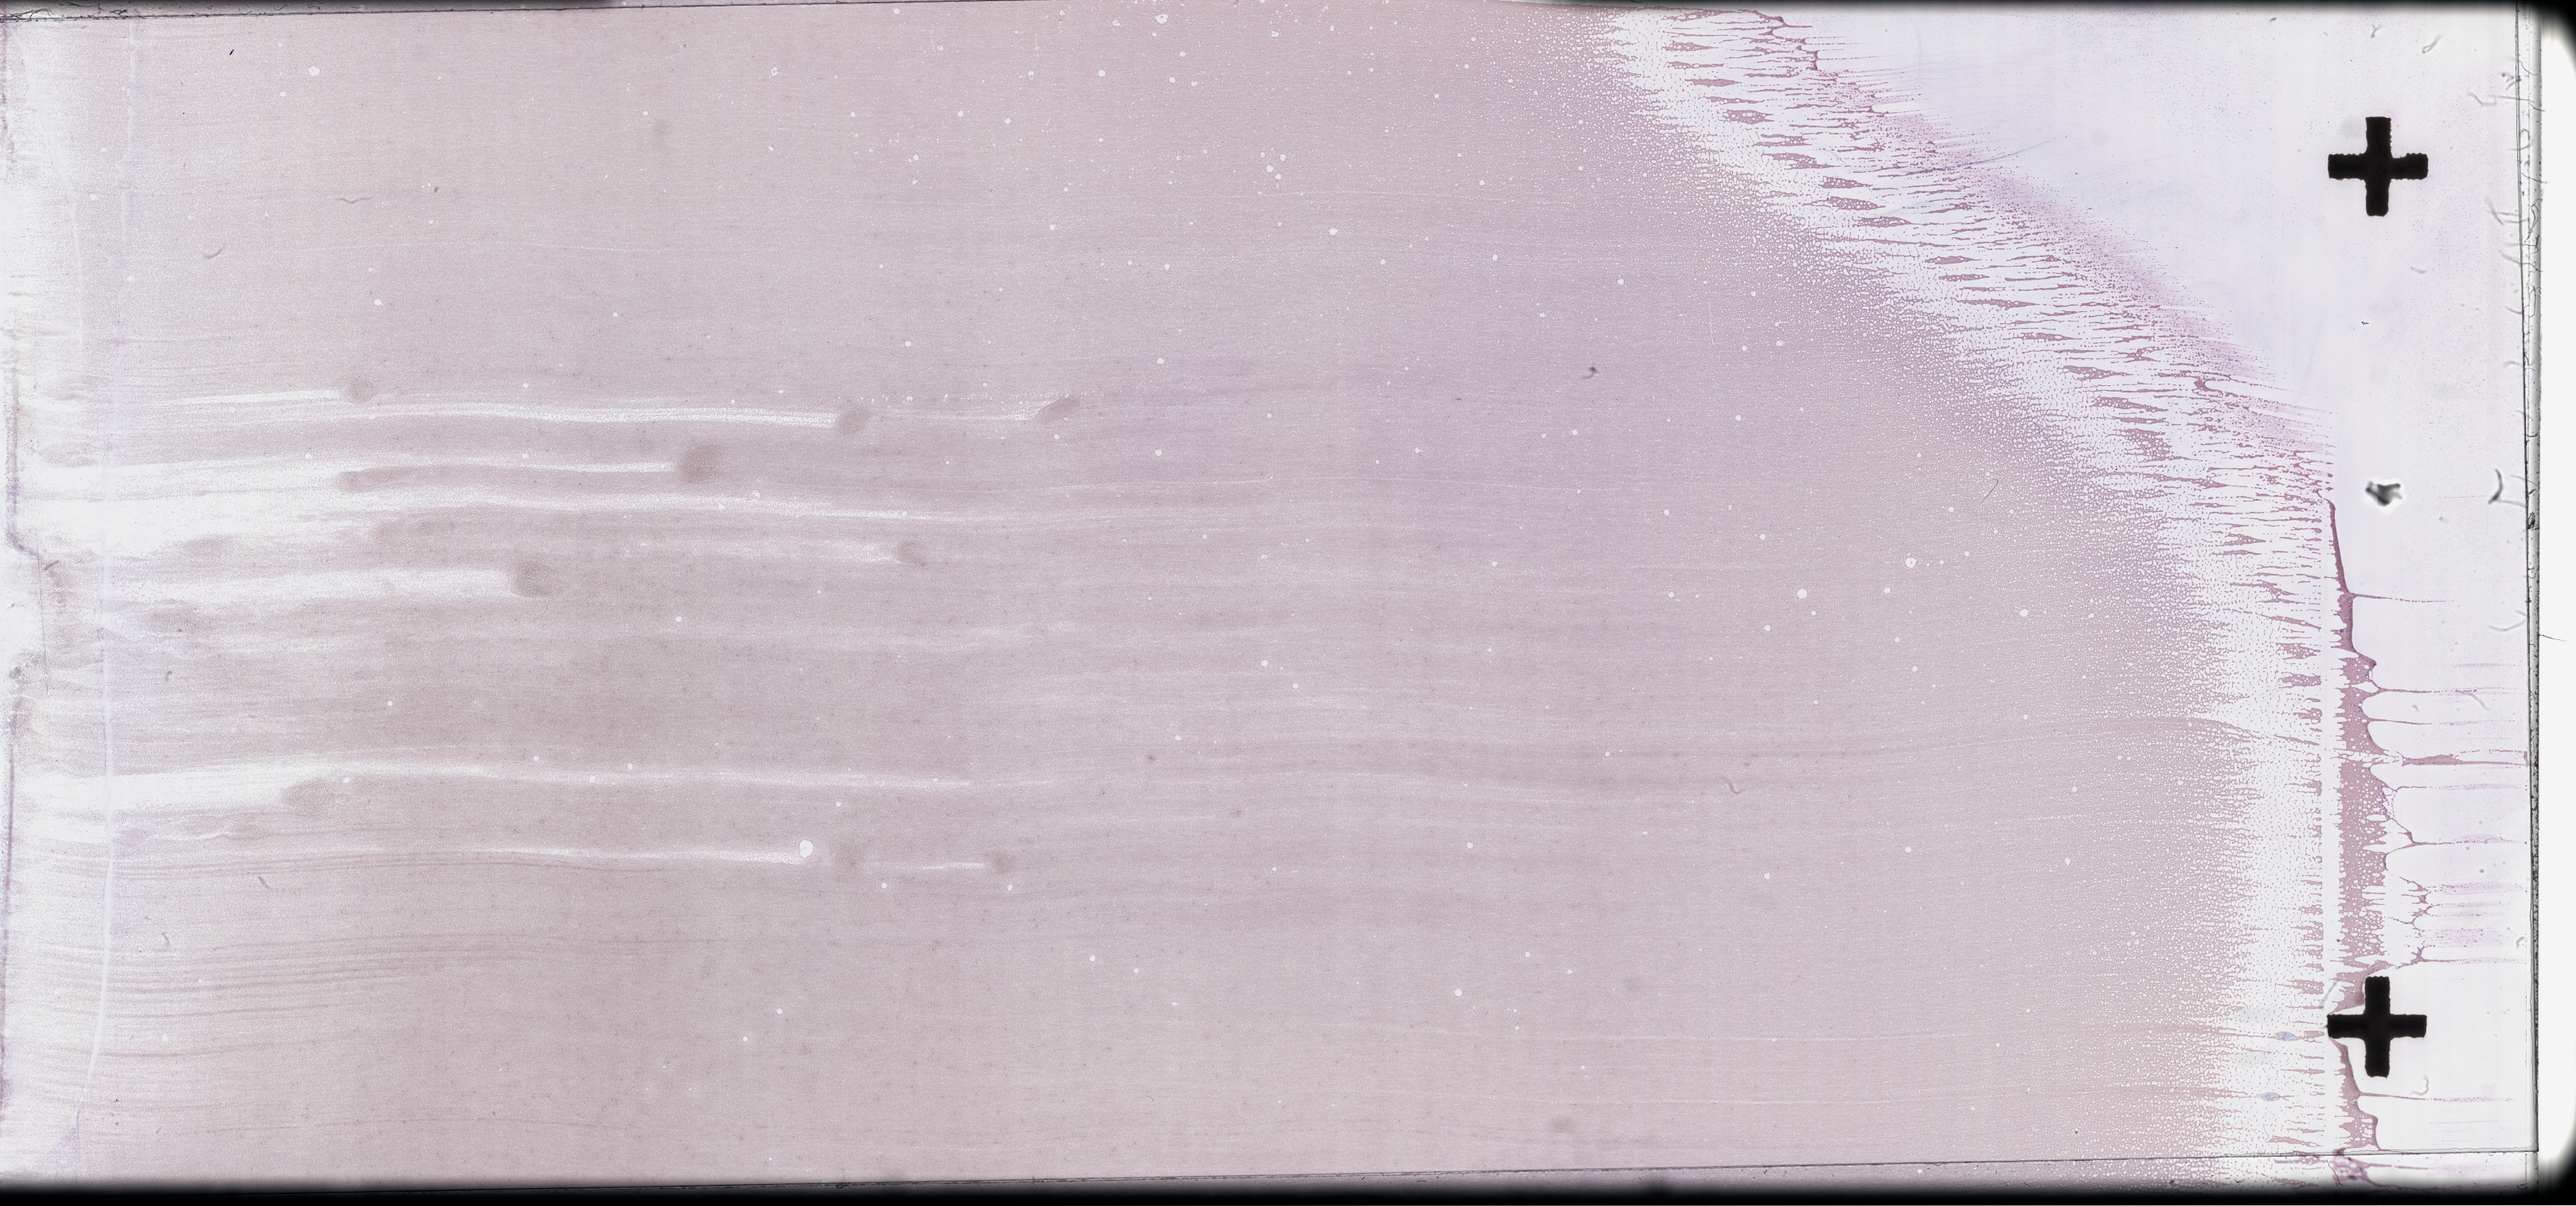
Whole-slide image of a whole blood smear, Wright-Giemsa stain — a low-resolution overview of the entire scanned area, about 52.3 x 24.5 mm. Patient: male.
From a patient with: Plasma Cell Myeloma.